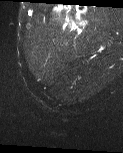
MRI of an extremity soft-tissue mass, one axial slice. Position 4 of 60 along the scan axis. T2-weighted fat-saturated. MR volume resampled by the dataset authors to the PET/CT grid (not the native acquisition matrix). 3.27 mm slice thickness. 123 × 153 image matrix, field of view 120 × 149 mm. Male patient. From the clinical record (not read from this slice): histological type: pleiomorphic liposarcoma; grade: high; site of the primary tumour: left thigh.
Outlined on this slice (expert contour drawn on MRI and transferred to this co-registered scan by the dataset authors):
- gross tumour volume including surrounding oedema: bounding box [x1, y1, x2, y2] px = [66, 24, 83, 34]